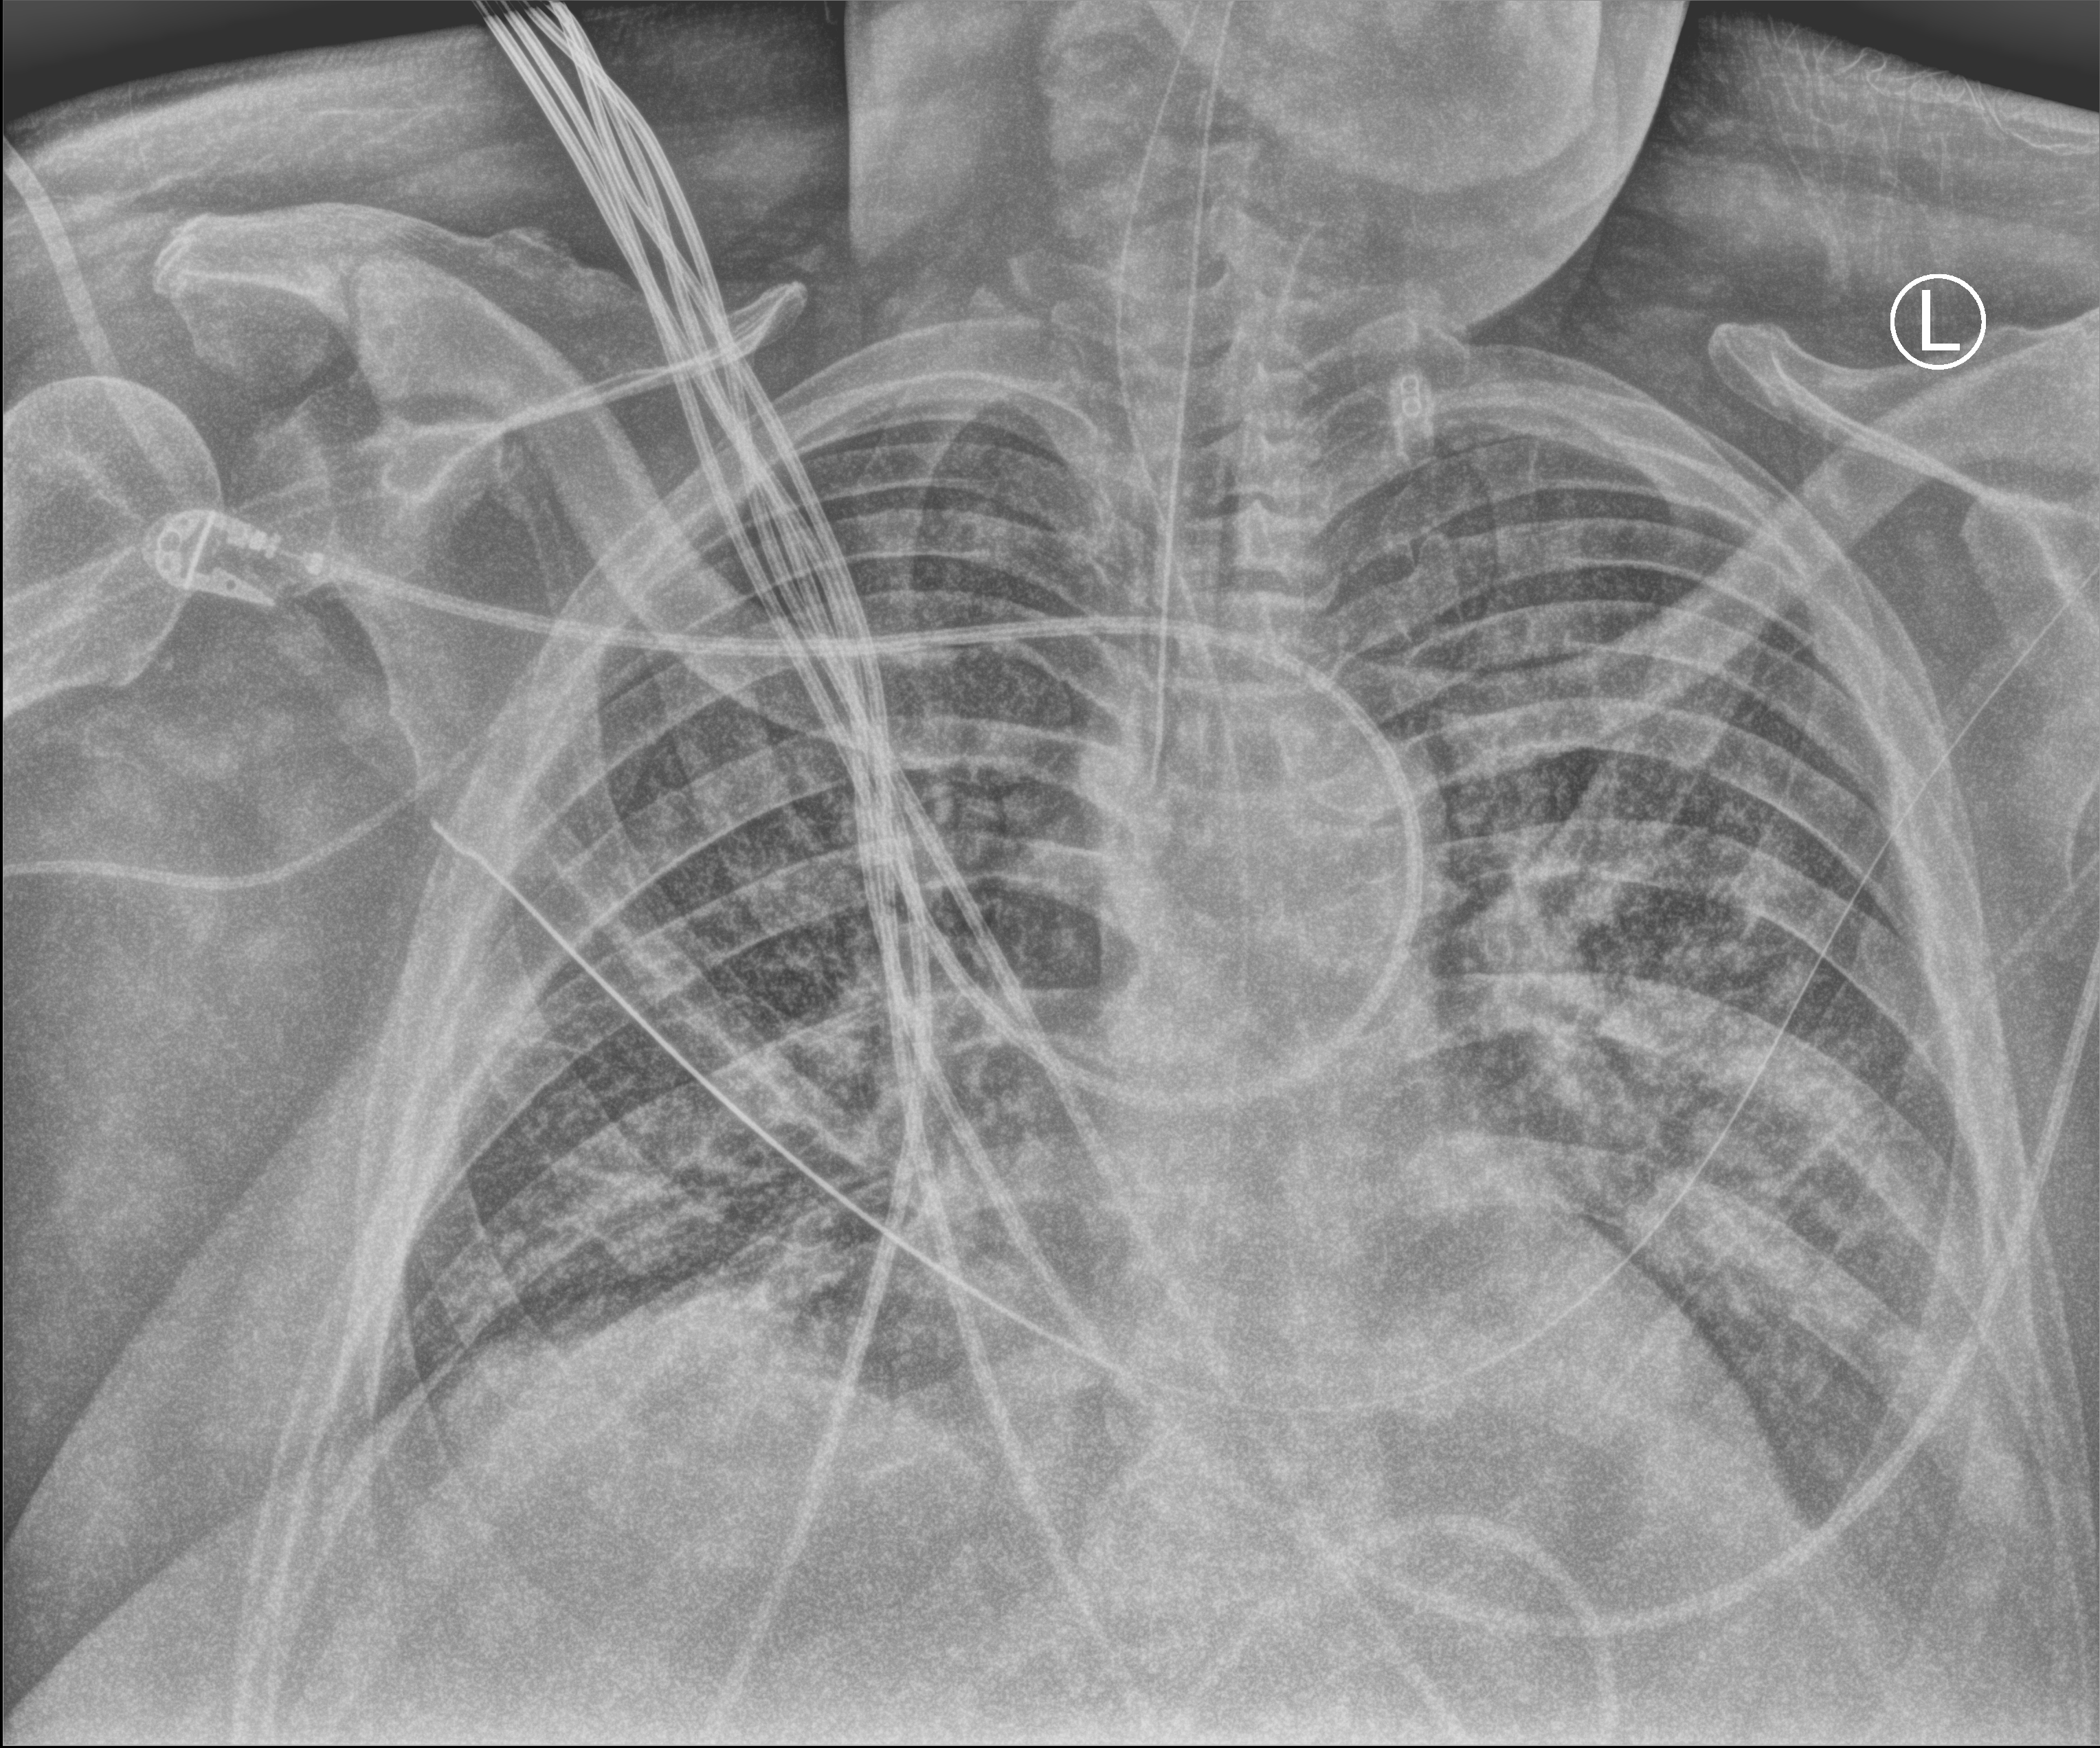
Portable chest radiograph; anteroposterior (AP) projection. Patient hospitalised with COVID-19; male, aged 60–74 years.
Hospital-stay facts (about this admission, not read from this image; timing relative to this image not recorded): COPD (admission record): no; mechanically ventilated during this hospital stay: yes.